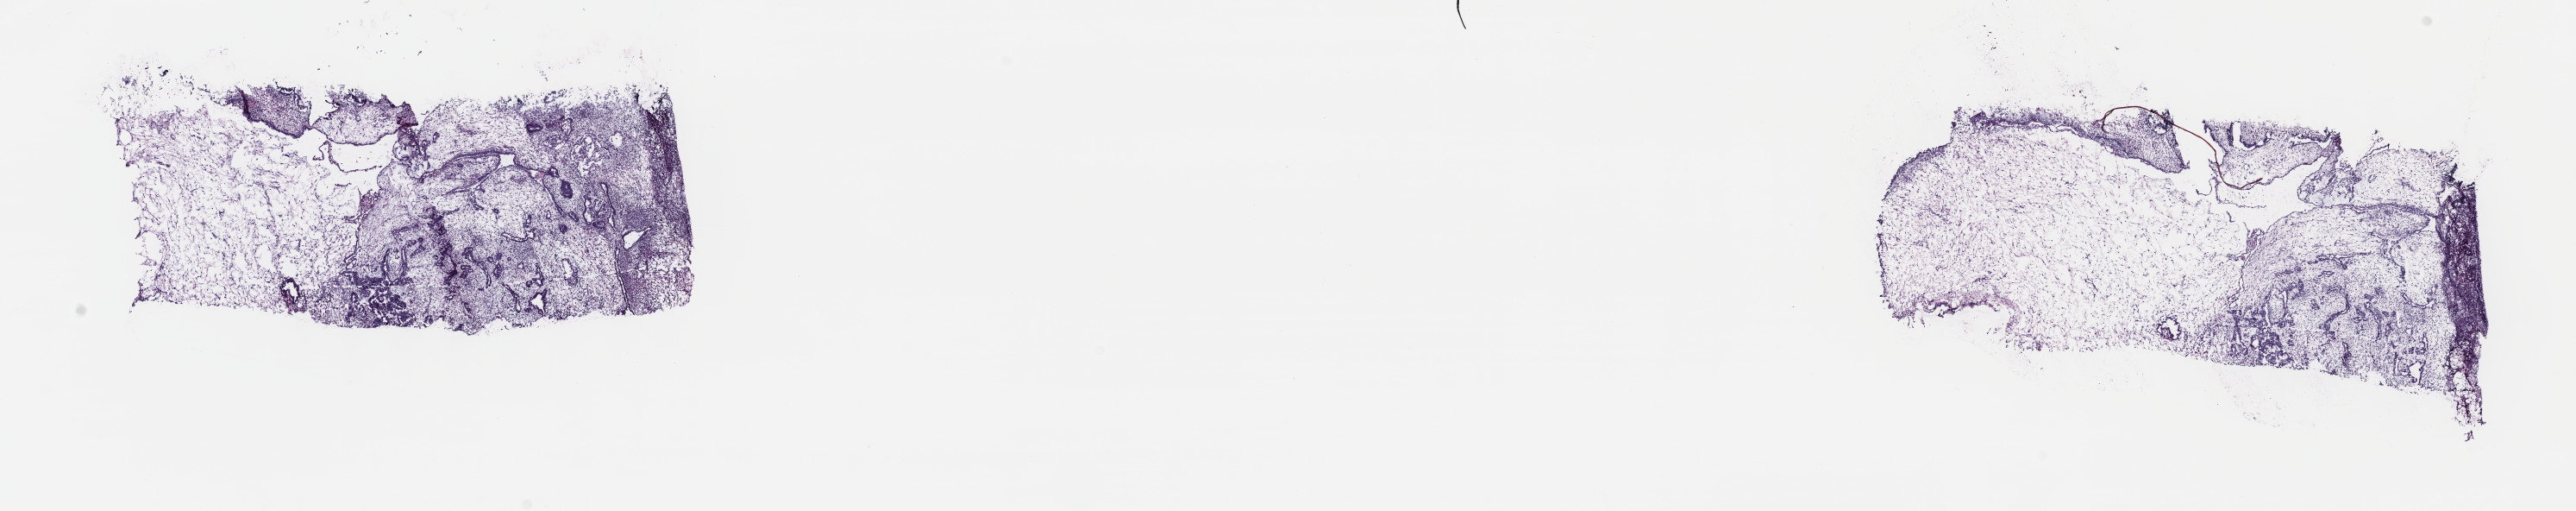
Whole-slide histology image, H&E-stained, shown as a low-resolution overview of the whole scanned area (about 24.2 x 4.8 mm, acquisition: 40x scan), frozen section from the top of the tissue portion, testis, primary tumour sample. Male patient; age at initial diagnosis 23 years. Slide review estimates, as recorded: tumour cells 60%, tumour nuclei 85%, normal cells 0%, stromal cells 40%, necrosis 0%. Infiltration values recorded for this section: lymphocyte infiltration 0%, monocyte infiltration 0%, neutrophil infiltration 0%.
Laterality: right. Diagnosis: Teratoma, malignant, NOS. AJCC pathologic stage: I (7th edition).